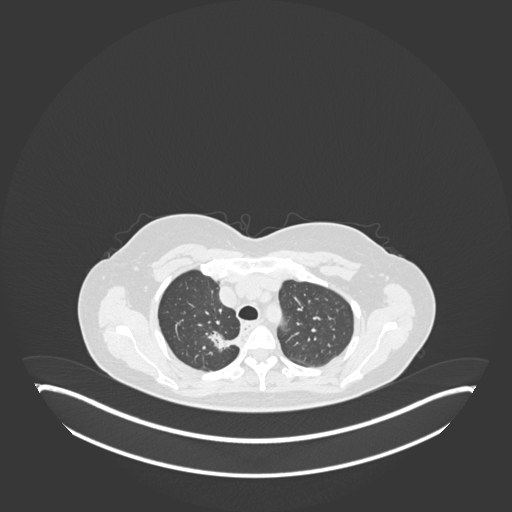
Chest CT, one axial slice. Position 139 of 181 along the scan axis. Reconstruction kernel B30f. Lung window (W 1500 / L -600 HU). 1 mm slice thickness. 512 × 512 image matrix, field of view 500 × 500 mm. Patient: female, 65 years. From the clinical record (not read from this slice): clinical TNM (as recorded): T1b N0 M0; histopathological grade: G2.
Structures marked on this image (rectangle marked by the reading radiologist):
- lung tumour (recorded histology: adenocarcinoma): bounding box (x1, y1, x2, y2) in pixels: (208, 329, 244, 354)